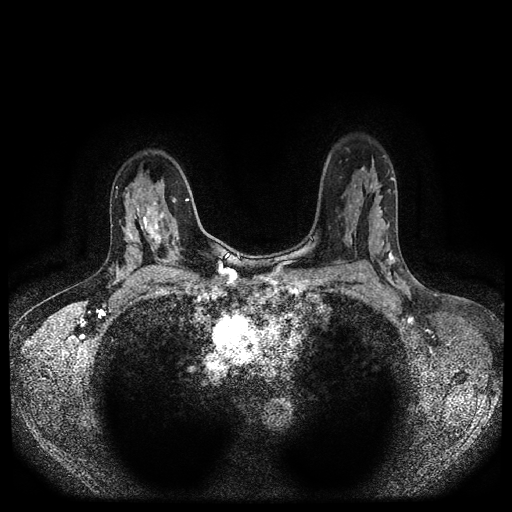
Breast MRI (dynamic contrast-enhanced, multi-phase), one axial slice. Position 69 of 116 along the scan axis. Dynamic contrast-enhanced series, time point 2 of 5 at this slice position (early post-contrast). 1.5 T. TE 2.6 ms, TR 5.4 ms. 512 × 512 image matrix, field of view 340 × 340 mm. Female patient, age 47 years.
Annotated regions visible in this slice (semi-automatically segmented with operator editing):
- breast lesion (labelled 'tumour' in the annotation; benign lesions carry a separate 'benign' label): bounding box <139,198,170,251> (left, top, right, bottom; pixels)